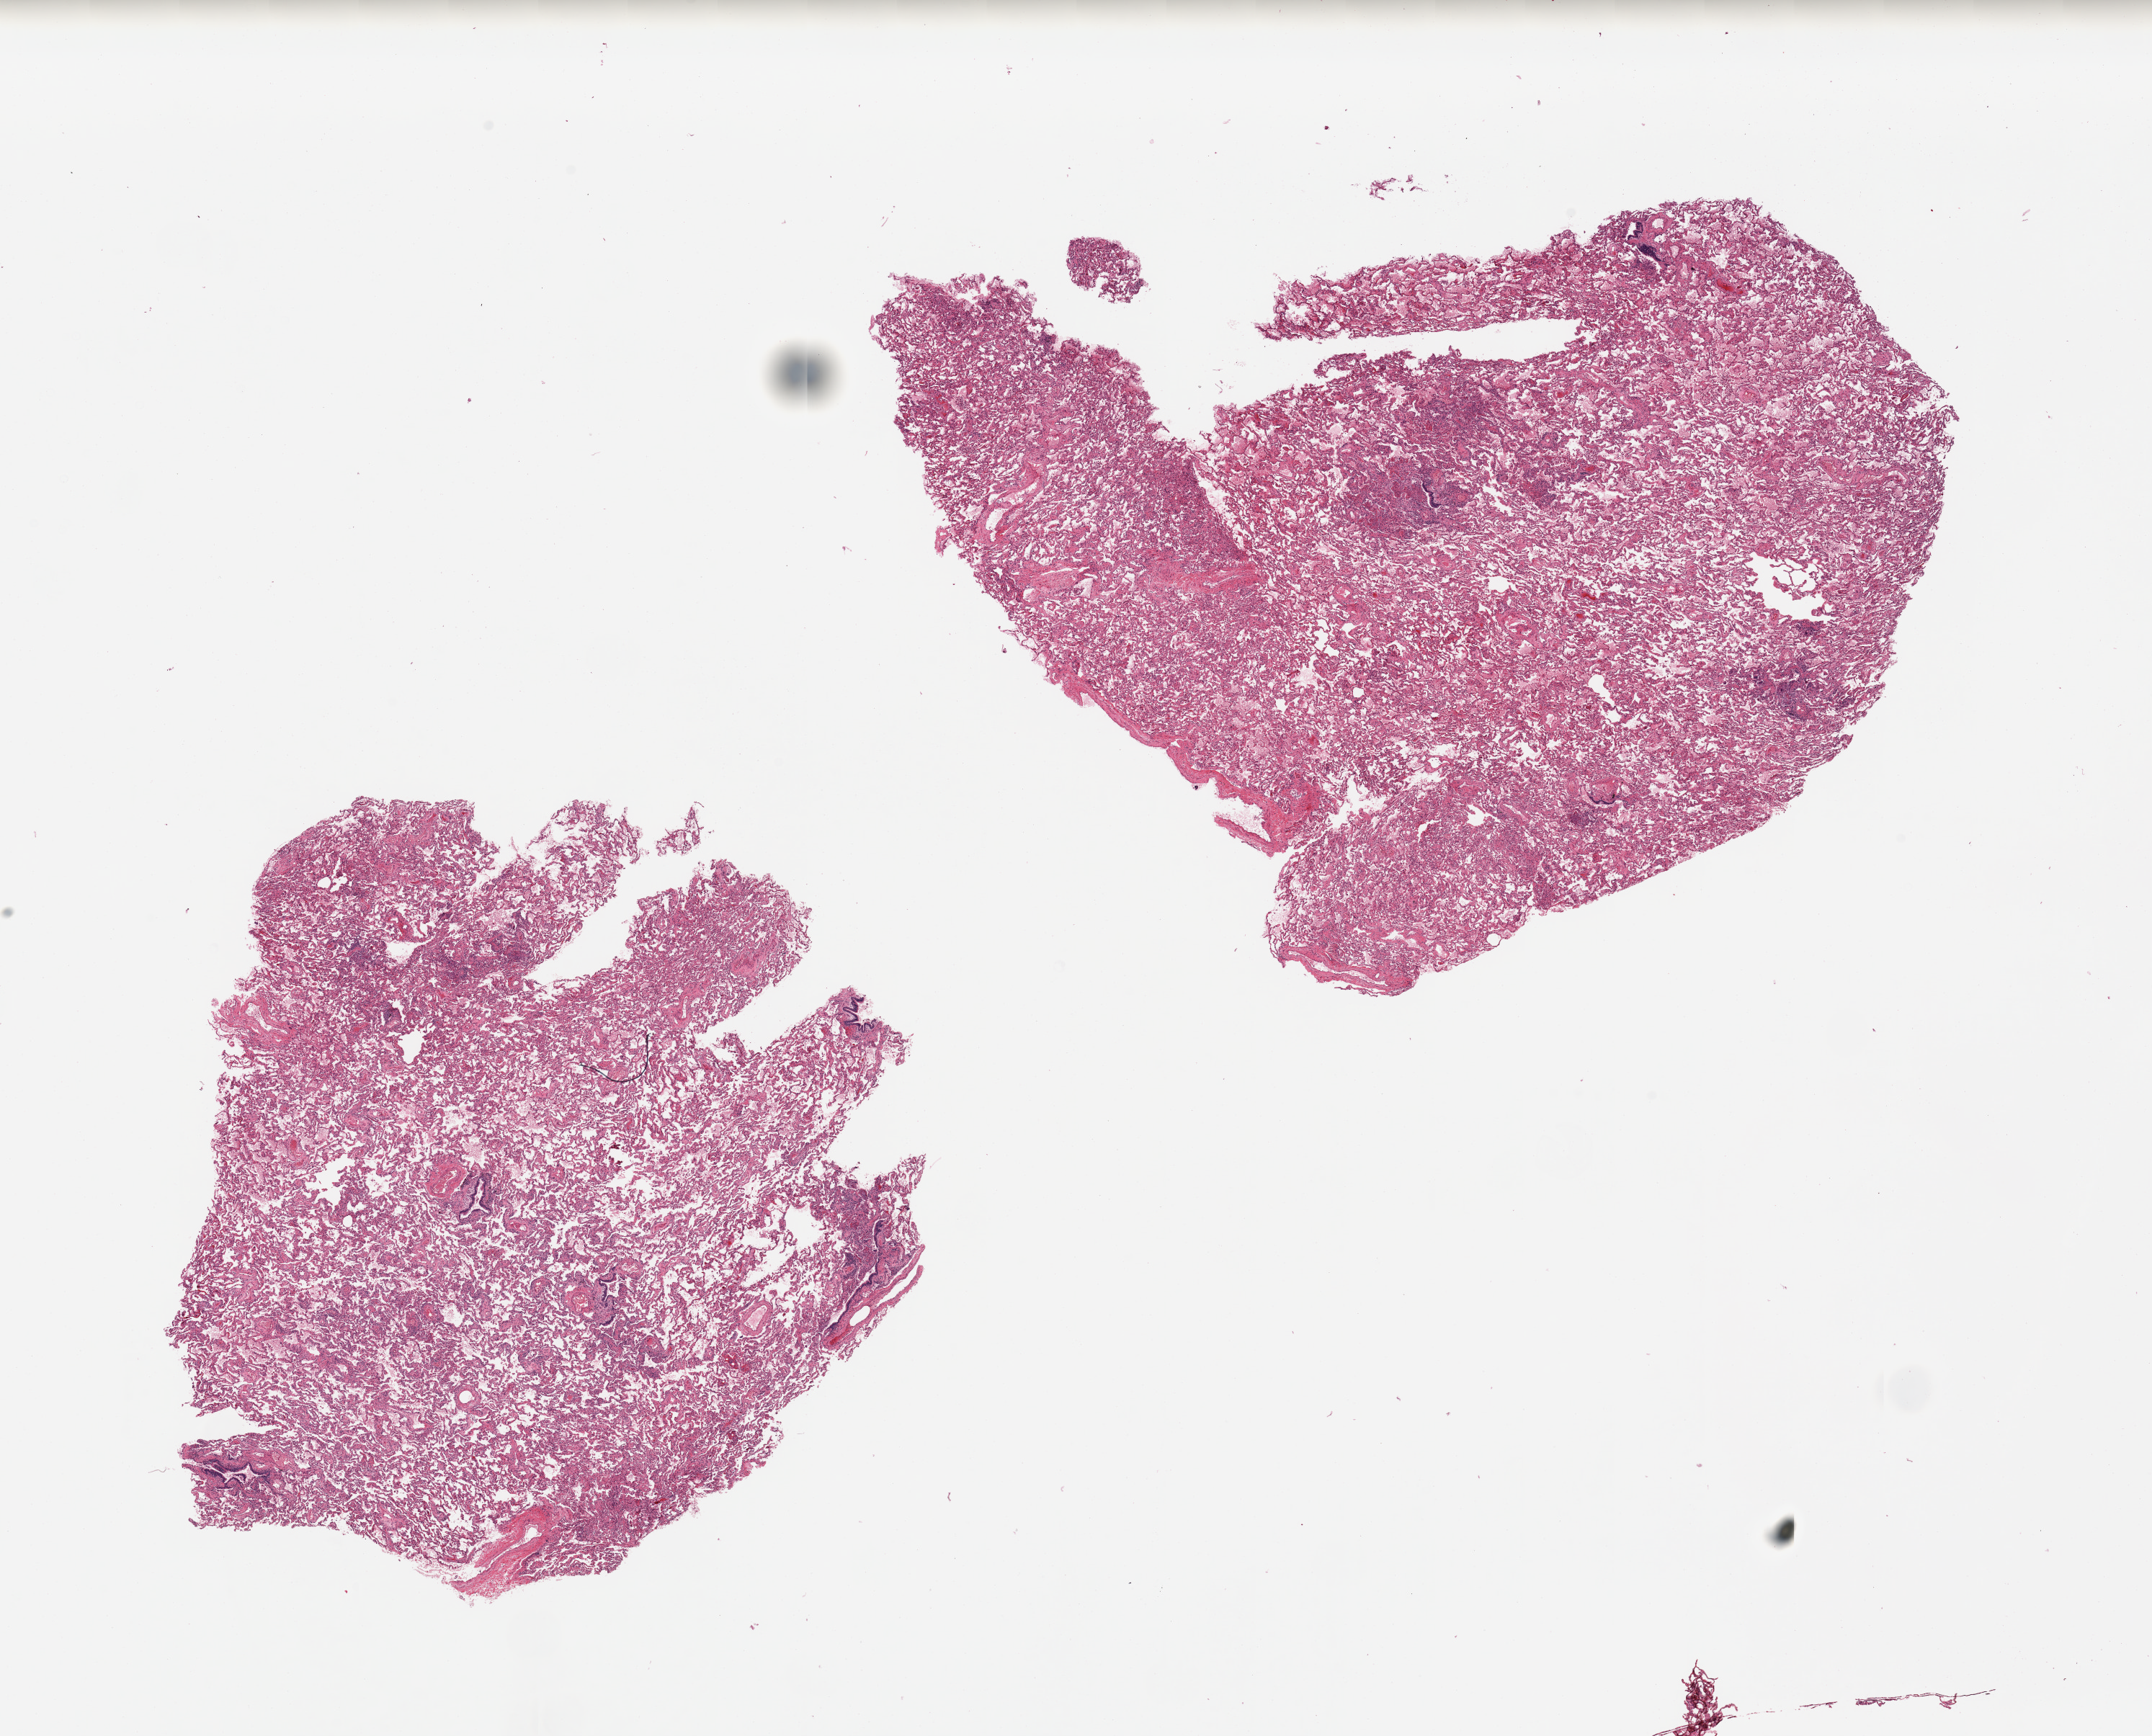
Whole-slide image, H&E stain, low-resolution overview of the scanned area, about 23.6 x 19.1 mm (acquisition: 20x scan), PAXgene-fixed paraffin-embedded (PFPE) section, section of lung (target tissue), tissue donor sample. Donor sex: female.
Pathologist's review note for this sample: 2 pieces. Patchy bronchopneumonia.